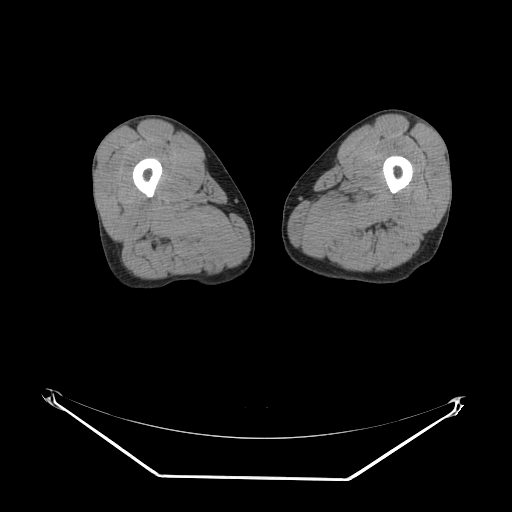
CT of an extremity soft-tissue mass (from a PET/CT study), one axial slice. Reconstruction kernel SOFT. 140 kVp. Soft-tissue window (W 400 / L 40 HU). 3.75 mm slice thickness. 512 × 512 image matrix, field of view 500 × 500 mm. Male patient. From the clinical record (not read from this slice): histological type: pleiomorphic liposarcoma; grade: high; site of the primary tumour: left thigh.
Structures marked on this image (expert contour drawn on MRI and transferred to this co-registered scan by the dataset authors):
- gross tumour volume including surrounding oedema: bounding box [x1, y1, x2, y2] px = [331, 203, 366, 223]